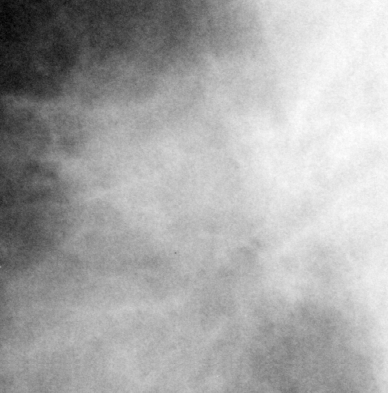
Crop from a digitized film mammogram around one marked abnormality, right breast, MLO view, BI-RADS breast density category 2 (scale 1–4).
Mass, shape irregular, margins spiculated; BI-RADS assessment category 5; pathology (as recorded): malignant.